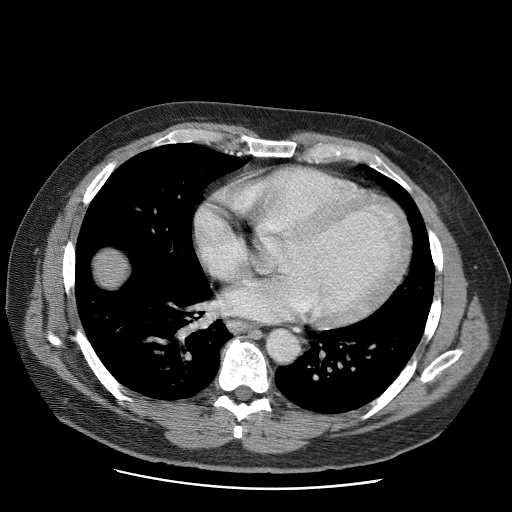
Contrast-enhanced abdominal CT (liver protocol), one axial slice; slice 71 of 81 in the series (ordered by position); 120 kVp; soft-tissue window (W 400 / L 40 HU); 512 × 512 image matrix, field of view 380 × 380 mm. Case-level facts recorded for this patient, not image findings: diagnosis: hepatocellular carcinoma (patient treated with transarterial chemoembolisation; whether this scan precedes or follows treatment is not stated here); TNM stage (as recorded): Stage-IIIA; Child-Pugh class: A; tumour size: 5.5 cm.
Structures marked on this image (semi-automatic segmentation, software-assisted and operator-edited):
- liver parenchyma outside the tumour (the mass and vessels are separate outlines, so this box may not span the whole liver): bounding box [x1, y1, x2, y2] px = [94, 249, 126, 286]